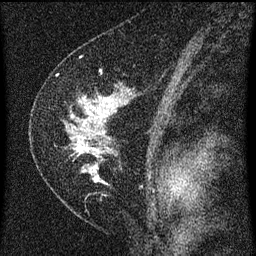
Breast MRI (dynamic contrast-enhanced), one sagittal slice. Position 40 of 60 along the scan axis. Dynamic contrast-enhanced series, image 2 of 3 at this slice position (ordered by acquisition). 1.5 T. TE 4.2 ms, TR 8 ms. 256 × 256 image matrix, field of view 180 × 180 mm. Patient: female, 47 years.
Structures marked on this image (semi-automatically segmented with operator editing):
- analysis volume of interest (the breast-tissue region the enhancement analysis was run in; not a lesion): bounding box (x1, y1, x2, y2) in pixels: (42, 82, 141, 193)
- tumour enhancement mask (voxels above the 70 % enhancement threshold inside the analysis volume of interest): (74, 98, 117, 183)